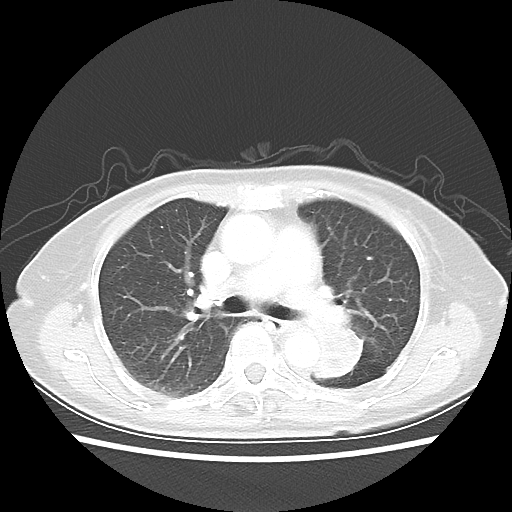
Chest CT, one axial slice. Position 31 of 50 along the scan axis. 80 kVp. Lung window (W 1500 / L -600 HU). 512 × 512 image matrix. Female patient, age 81 years. Case-level facts recorded for this patient, not image findings: clinical TNM (as recorded): T2 N0 M1a.
Structures marked on this image (rectangle marked by the reading radiologist):
- lung tumour (recorded histology: squamous cell carcinoma): bounding box <310,317,365,383> (left, top, right, bottom; pixels)